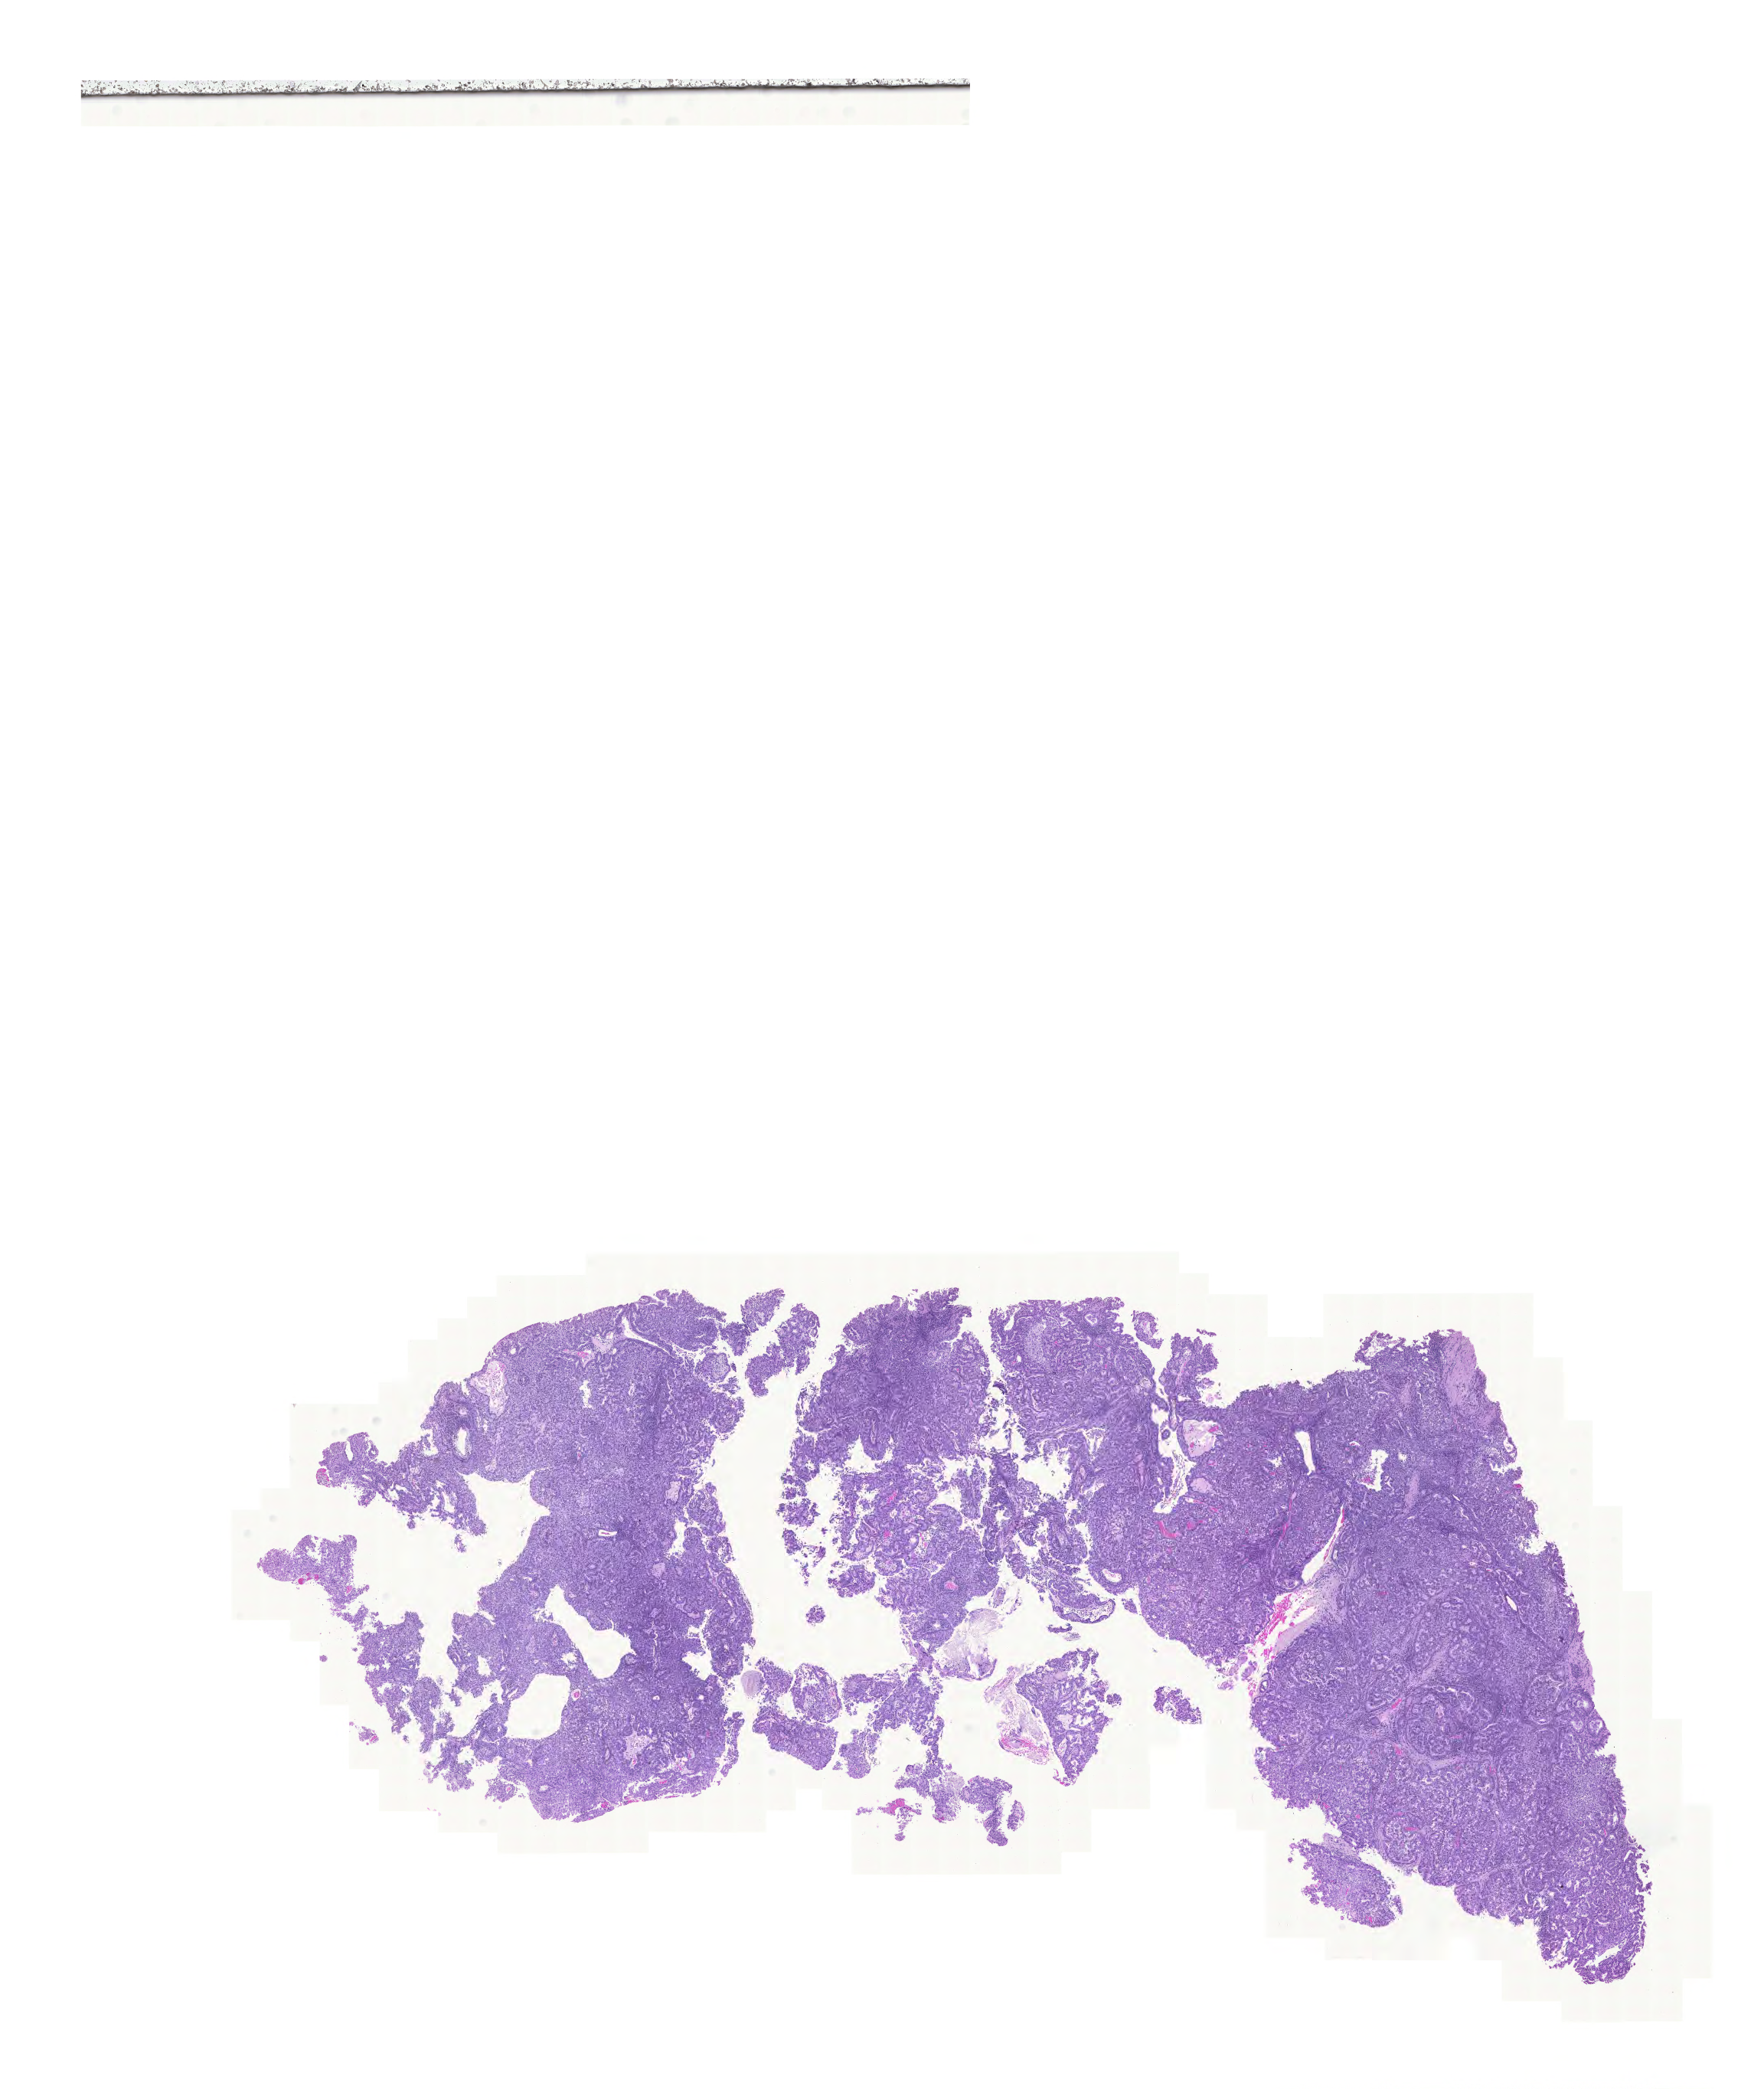
Digitized Hematoxylin and eosin (H&E) stained tissue section (whole slide), shown as a low-resolution overview of the whole scanned area (about 17.1 x 20.3 mm, acquisition: 20x scan); FFPE section; primary tumour sample from the lung. Male, age 68 years at initial diagnosis.
- TNM: T2 N0 M0
- AJCC pathologic stage: IB (6th edition)
- laterality: left
- pathologic diagnosis: Adenocarcinoma with mixed subtypes (lower lobe, lung)